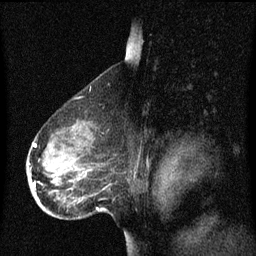
Breast MRI (dynamic contrast-enhanced), one sagittal slice. Slice 45 of 60 in the series (ordered by position). Dynamic contrast-enhanced series, image 2 of 3 at this slice position (ordered by acquisition). 1.5 T. TE 4.2 ms, TR 8.4 ms. 256 × 256 image matrix, field of view 200 × 200 mm. Female patient, age 49 years. Case-level facts recorded for this patient, not image findings: setting: breast cancer imaged before/during neoadjuvant chemotherapy; receptor status: HR-positive, HER2-negative.
Outlined on this slice (semi-automatically segmented with operator editing):
- analysis volume of interest (the breast-tissue region the enhancement analysis was run in; not a lesion): bounding box [x1, y1, x2, y2] px = [28, 126, 94, 201]
- tumour enhancement mask (voxels above the 70 % enhancement threshold inside the analysis volume of interest): [33, 144, 38, 187]